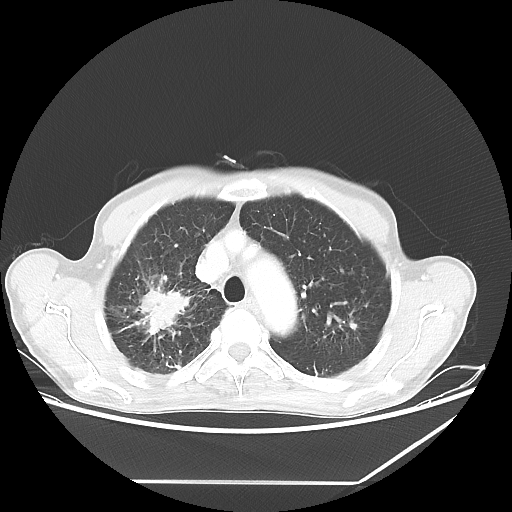
Chest CT, one axial slice; slice 49 of 65 in the series (ordered by position); 80 kVp; lung window (W 1500 / L -600 HU); 512 × 512 image matrix, field of view 397 × 397 mm. Patient: male, 68 years. Case-level facts recorded for this patient, not image findings: clinical TNM (as recorded): T3 N3 M0.
Outlined on this slice (bounding box drawn by a radiologist):
- lung tumour (recorded histology: adenocarcinoma): bounding box (x1, y1, x2, y2) in pixels: (131, 280, 197, 351)